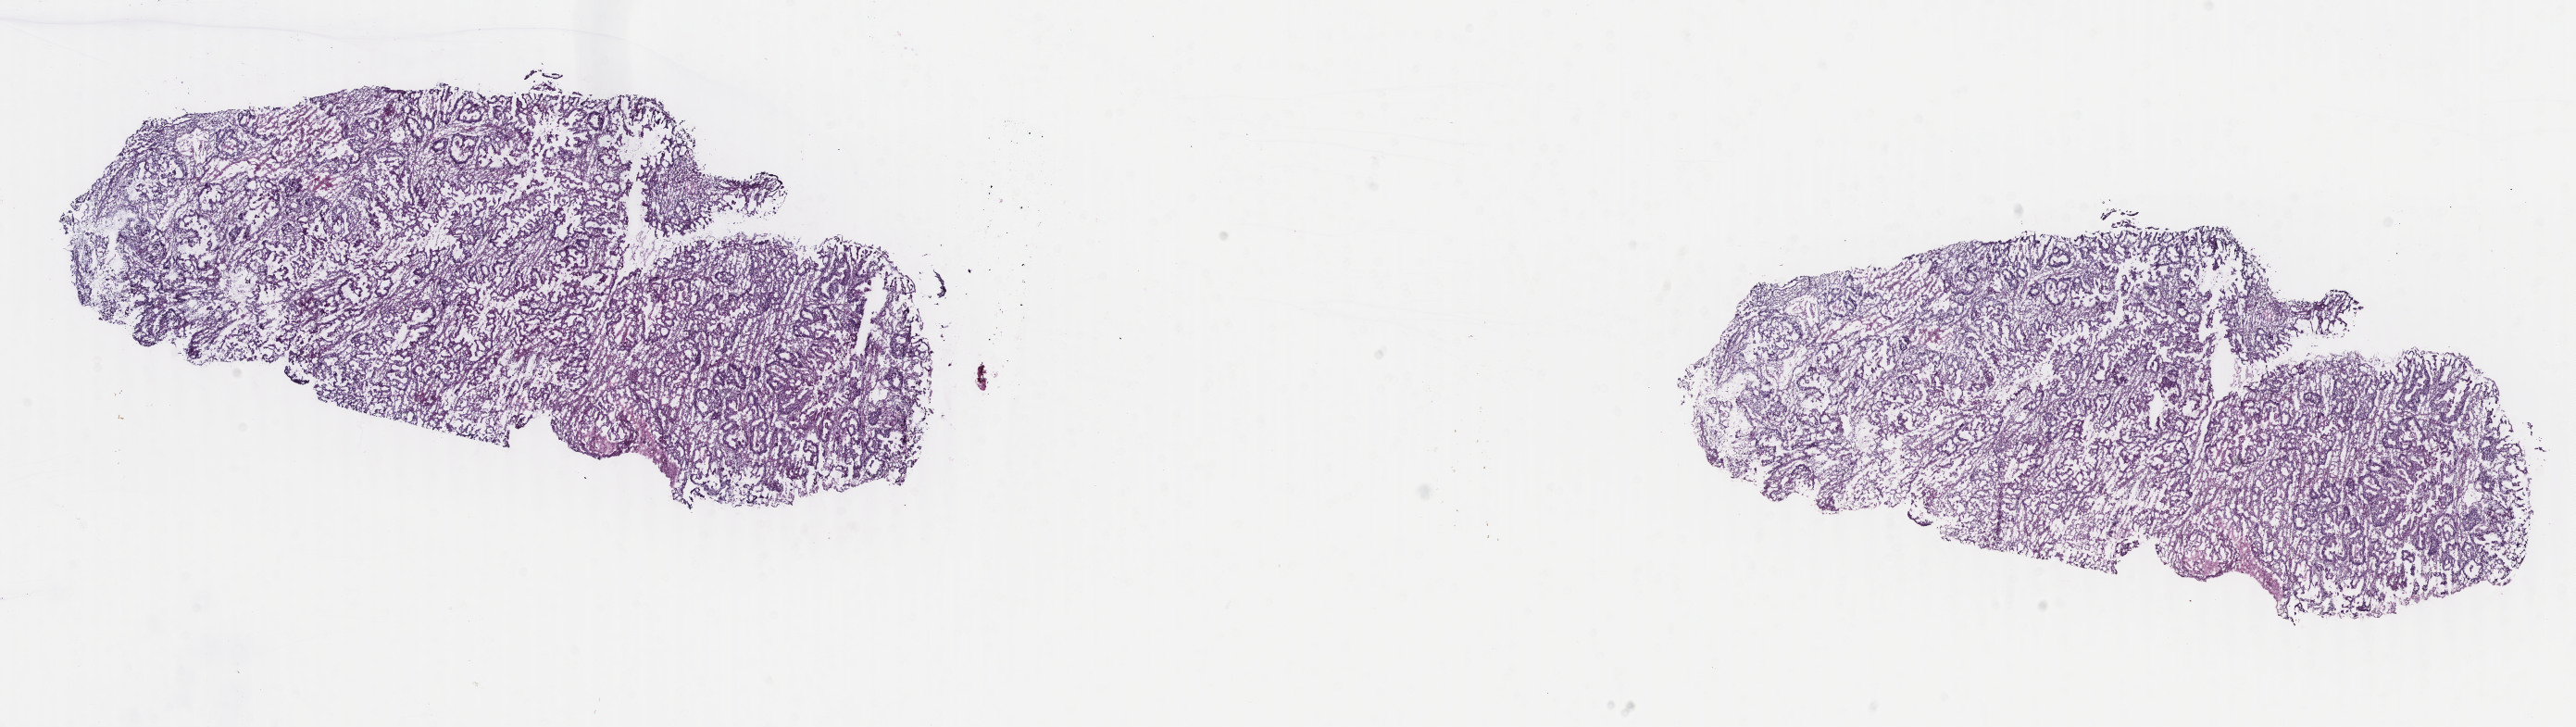
Digitized H&E tissue section (whole slide) — whole scanned area (about 22.1 x 6.2 mm, slide scanned at 40x) shown as a low-resolution overview, frozen section from the top of the tissue portion, sample: primary tumour, uterus. Female, age 62 years at initial diagnosis. Histologic grade: G1 (well differentiated). Slide review estimates, as recorded: tumour cells 82%, tumour nuclei 90%, normal cells 0%, stromal cells 10%, necrosis 8%. Inflammatory infiltration, as recorded: lymphocyte infiltration 20%, monocyte infiltration 8%, neutrophil infiltration 5%.
- FIGO stage: IA
- pathologic diagnosis: Endometrioid adenocarcinoma, NOS (endometrium)